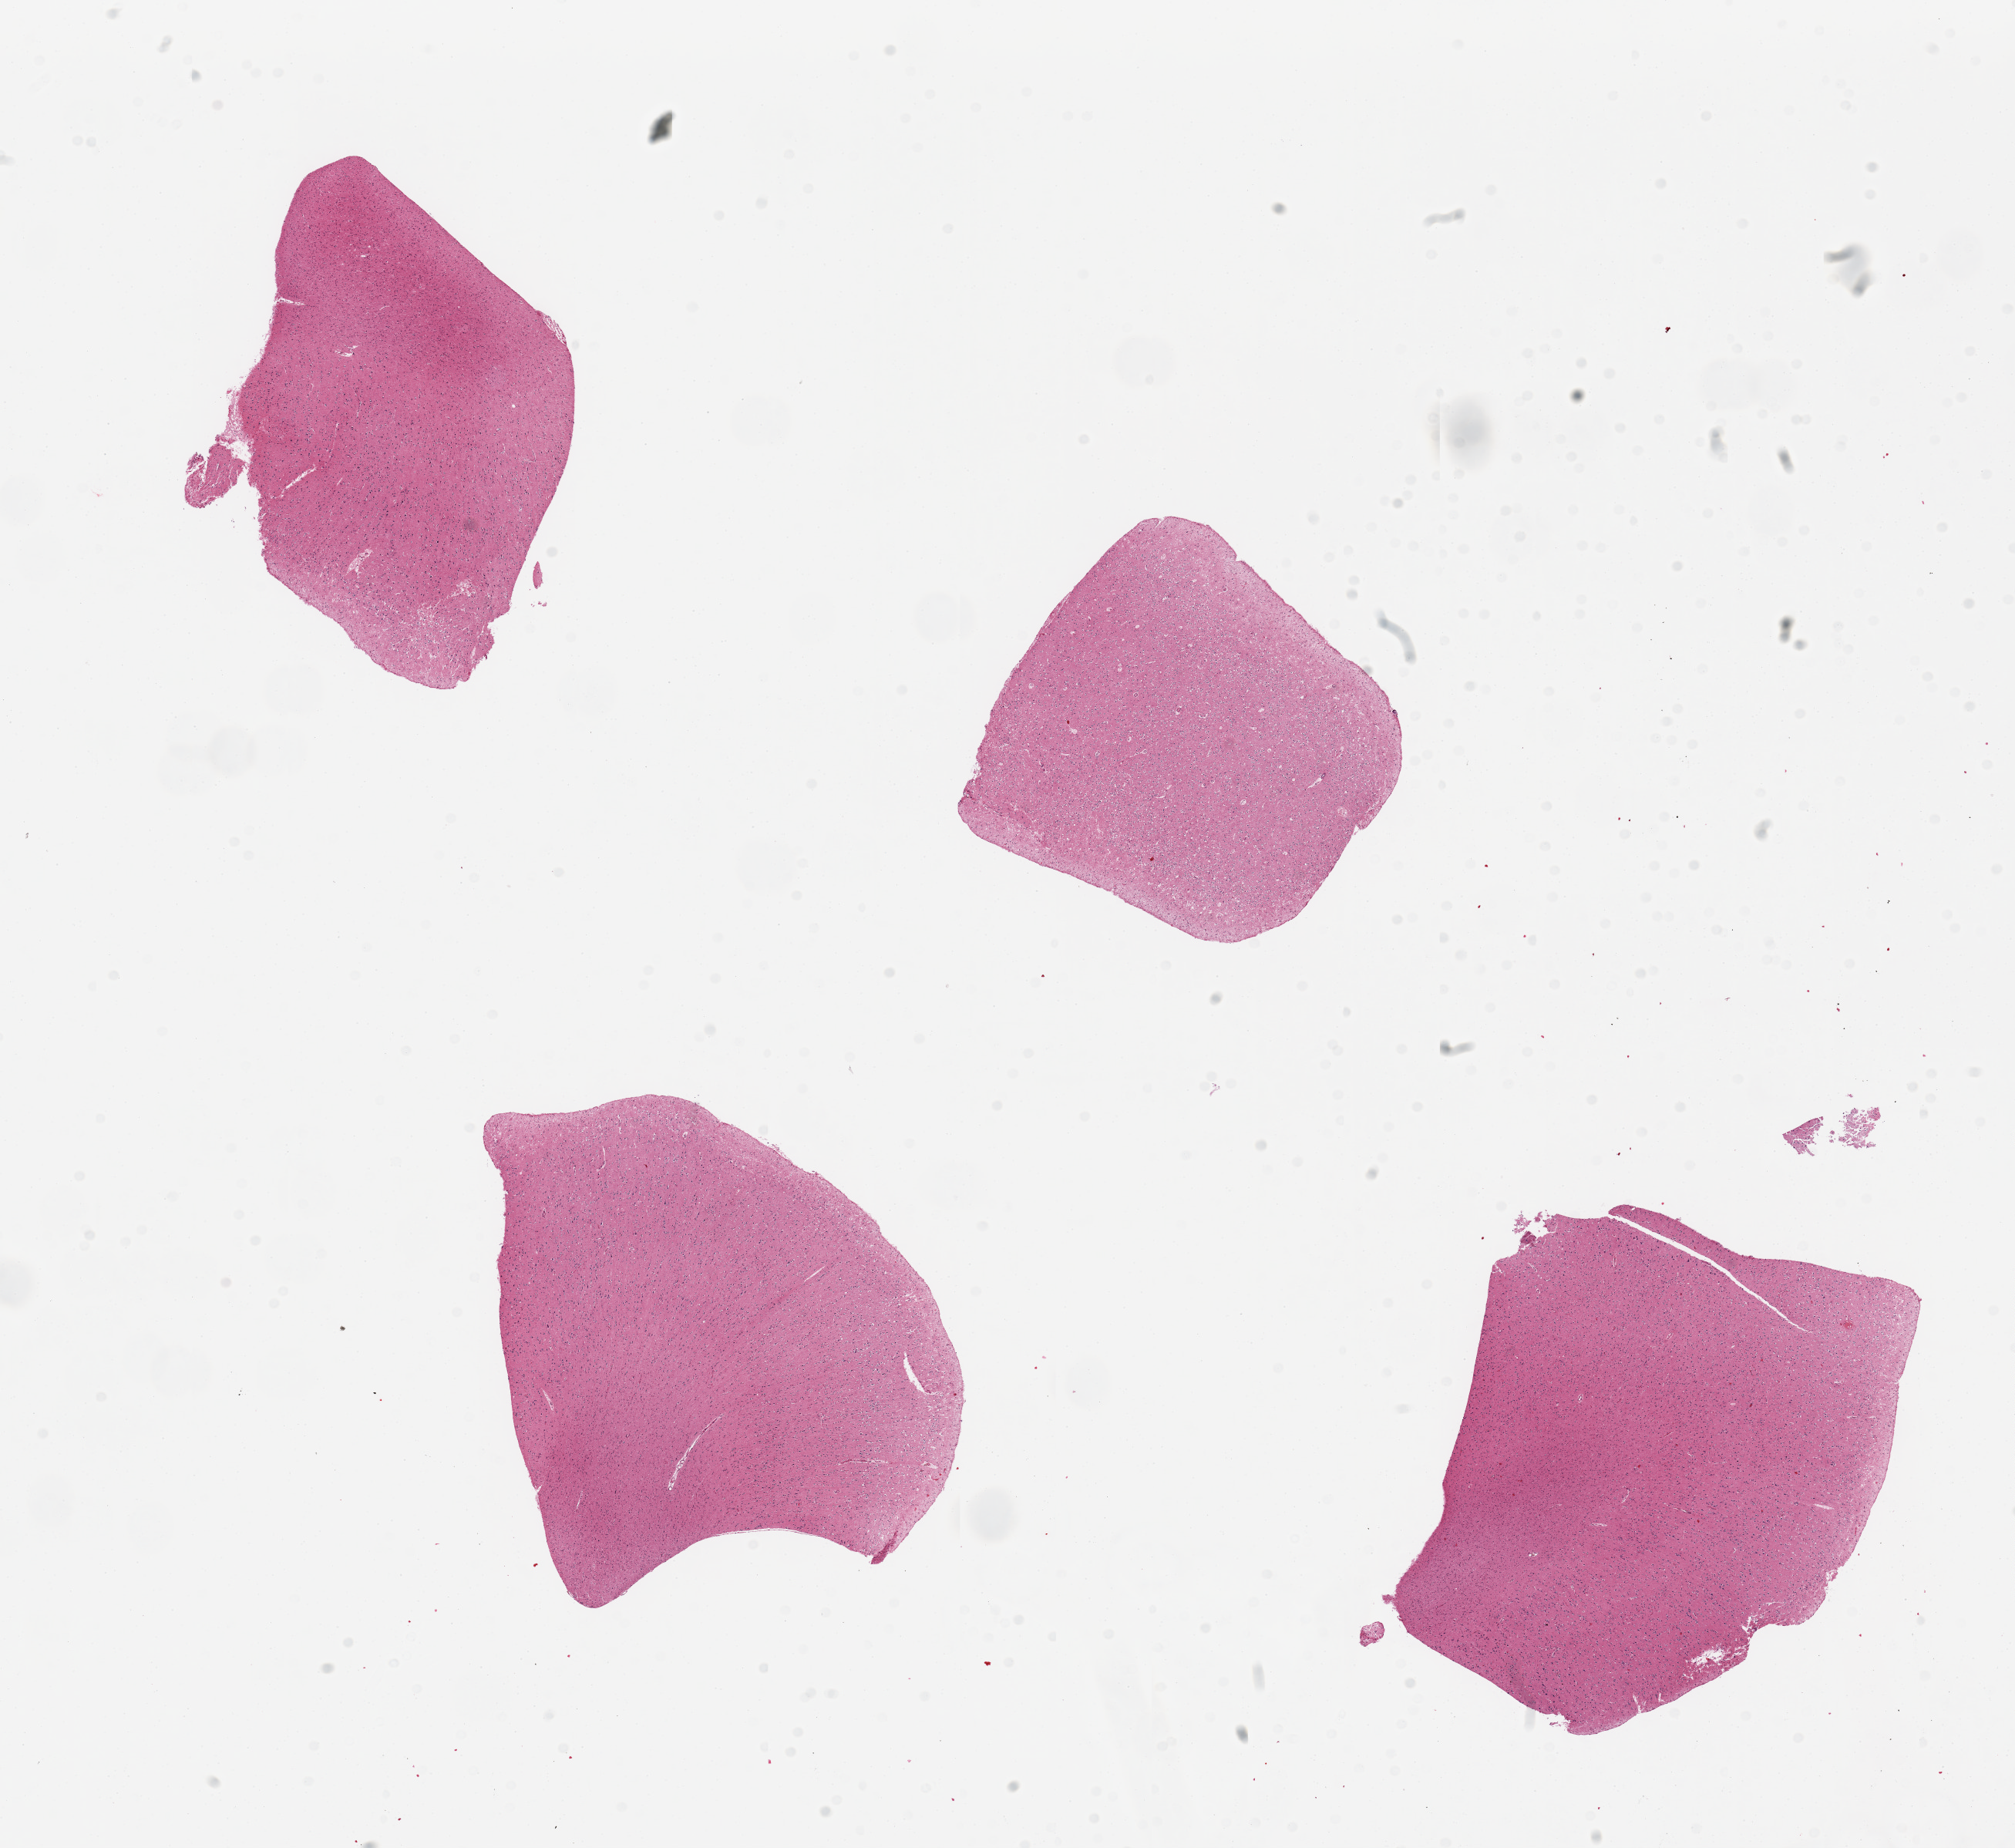
Digitized H&E-stained section — low-resolution overview of the scanned area, about 20.7 x 19.0 mm (from a 20x scan), PAXgene-fixed, paraffin-embedded tissue, sampled site (target tissue): cerebral cortex, donor tissue sample. Donor: male.
• review note (as recorded): 4 pieces, no significant abnormalities